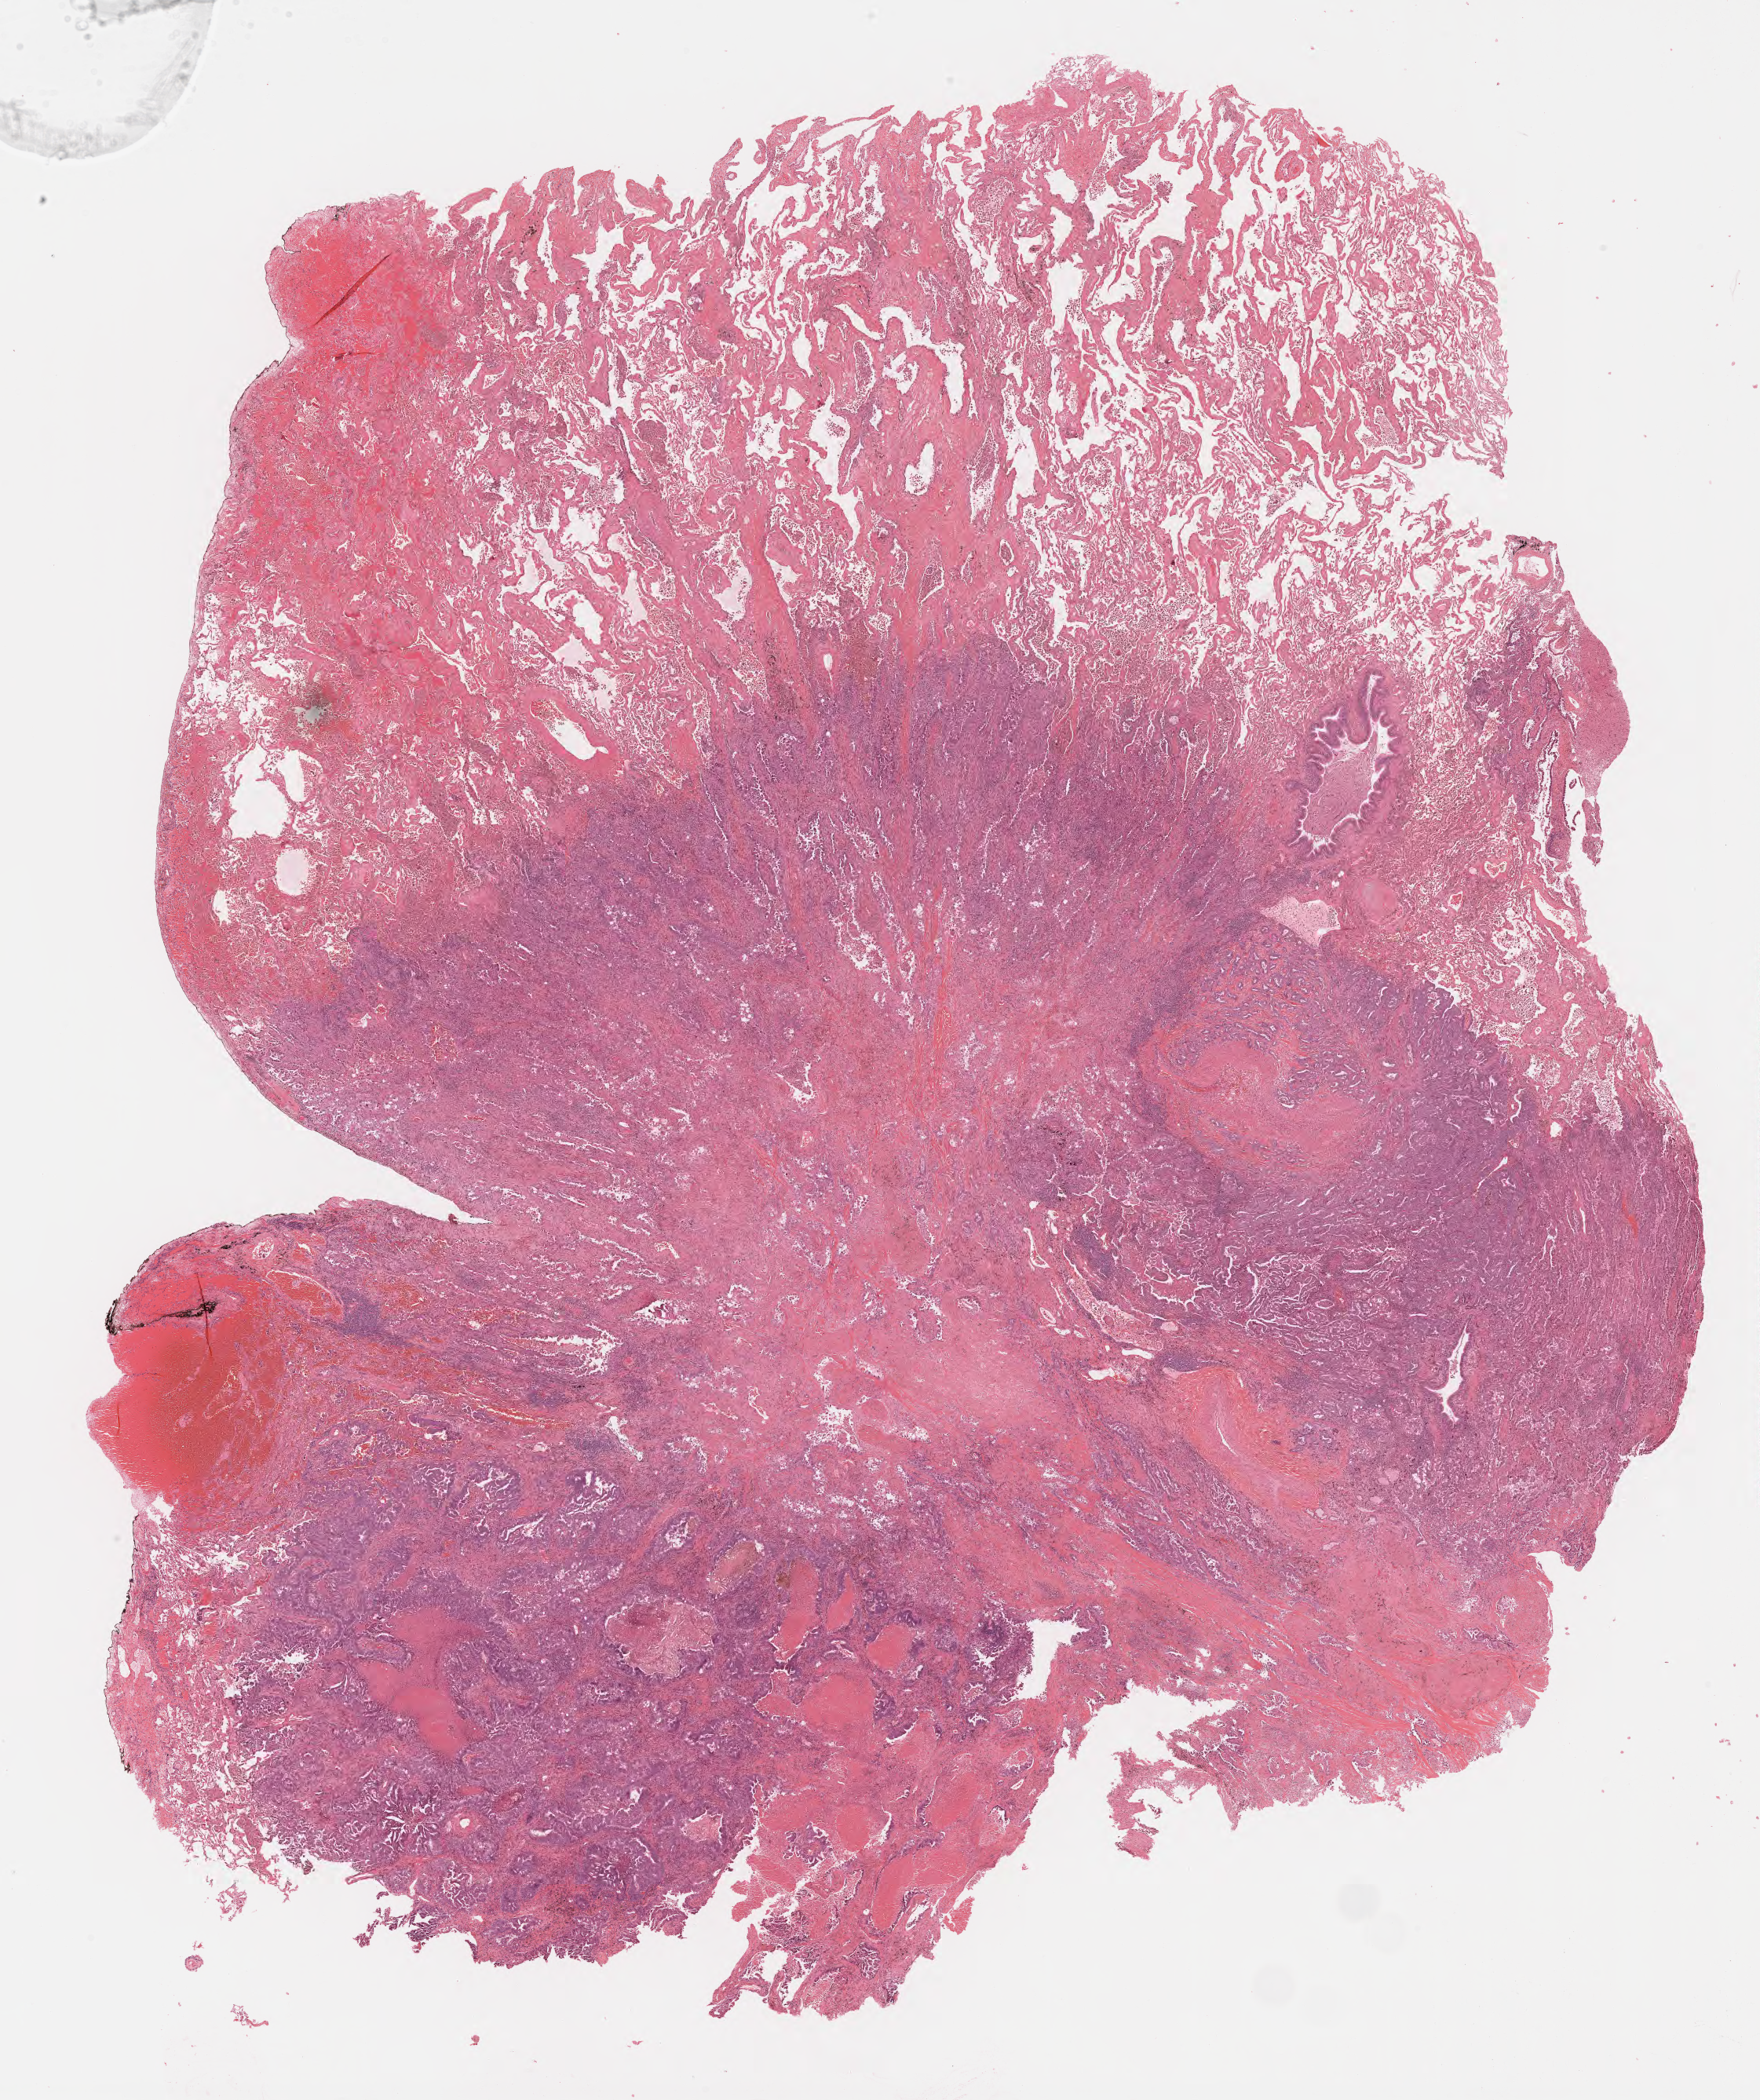
Digitized H&E-stained tissue section (whole slide), a low-resolution overview of the entire scanned area, about 18.1 x 21.6 mm. FFPE section. Sample: primary tumour, lung. Male, age 67 years at initial diagnosis.
Laterality: left. Histologic diagnosis: Adenocarcinoma, NOS (lower lobe, lung). AJCC pathologic stage: IB (5th edition).